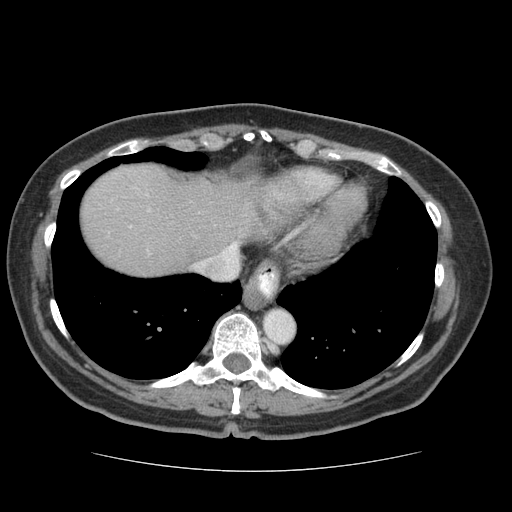
Contrast-enhanced abdominal CT (liver protocol), one axial slice. Position 64 of 75 along the scan axis. 140 kVp. Soft-tissue window (W 400 / L 40 HU). 512 × 512 image matrix, field of view 360 × 360 mm. Case-level facts recorded for this patient, not image findings: diagnosis: hepatocellular carcinoma (patient treated with transarterial chemoembolisation; whether this scan precedes or follows treatment is not stated here); TNM stage (as recorded): Stage-I; Child-Pugh class: A; tumour differentiation: moderately differentiated; tumour nodularity: uninodular.
Outlined on this slice (semi-automatic segmentation, software-assisted and operator-edited):
- liver parenchyma outside the tumour (the mass and vessels are separate outlines, so this box may not span the whole liver): bounding box (x1, y1, x2, y2) in pixels: (80, 164, 260, 276)
- liver vessels: (130, 226, 237, 245)